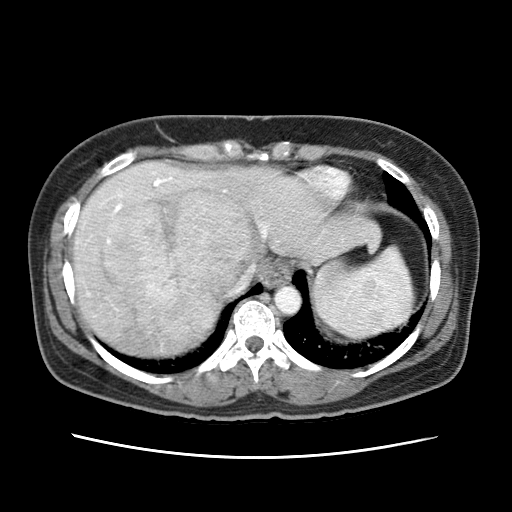
Contrast-enhanced abdominal CT (liver protocol), one axial slice. Position 56 of 79 along the scan axis. 120 kVp. Soft-tissue window (W 400 / L 40 HU). 2.5 mm slice thickness. 512 × 512 image matrix, field of view 340 × 340 mm. Case-level facts recorded for this patient, not image findings: diagnosis: hepatocellular carcinoma (patient treated with transarterial chemoembolisation; whether this scan precedes or follows treatment is not stated here); TNM stage (as recorded): Stage-I; Child-Pugh class: A; tumour differentiation: moderately differentiated.
Structures marked on this image (semi-automatic segmentation, software-assisted and operator-edited):
- abdominal aorta: bounding box [x1, y1, x2, y2] px = [273, 285, 300, 314]
- liver parenchyma outside the tumour (the mass and vessels are separate outlines, so this box may not span the whole liver): [72, 162, 380, 356]
- mass: [103, 186, 256, 342]
- liver vessels: [114, 172, 267, 236]